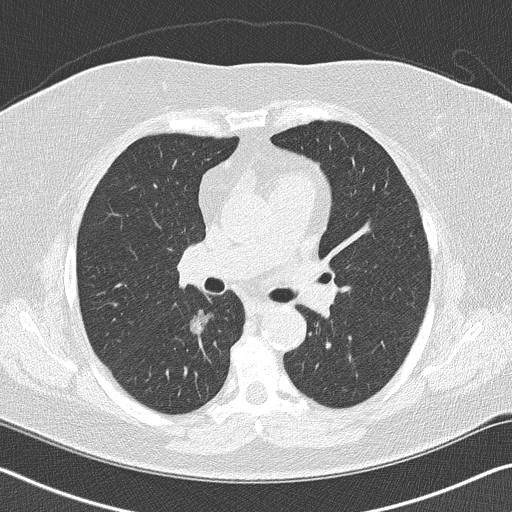
Low-dose screening chest CT, axial slice. First (baseline) screen. Lung window (W 1500 / L -600 HU). 2 mm slice thickness. Slice 57 of 146 in the series. Female, age 60 years at enrolment. Former smoker at enrolment.
Lesion marked by an expert reader, bounding box [x1, y1, x2, y2] px = [175, 298, 227, 347]. The screening reader recorded 2 non-calcified nodules or masses ≥4 mm on this exam (right lower lobe, left upper lobe); which of them this box marks is not recorded. Official screen result: positive, change unspecified: nodule(s) >= 4 mm or enlarging nodule(s), mass(es), or other non-specific abnormalities suspicious for lung cancer. Participant outcome: lung cancer diagnosed 482 days after this screen — bronchiolo-alveolar carcinoma, non-mucinous, right lower lobe, stage IA (AJCC 6th edition), 15 mm at pathology.